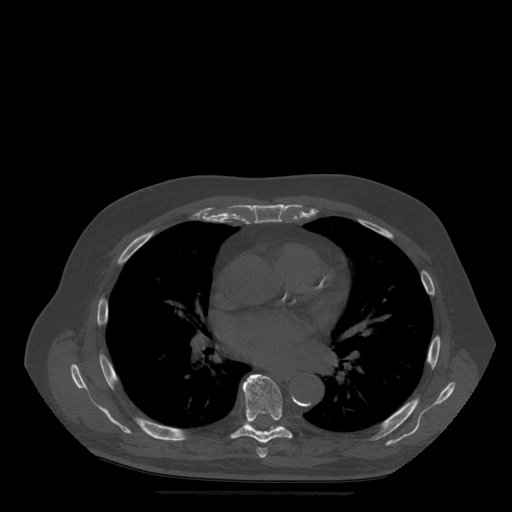
CT including the spine, one axial slice; bone window (W 1800 / L 400 HU); 512 × 512 image matrix, field of view 420 × 420 mm. Patient age 72 years. Case-level facts recorded for this patient, not image findings: primary cancer: prostate.
Outlined on this slice (semi-automatically segmented with operator editing):
- T6 vertebra: bounding box (x1, y1, x2, y2) in pixels: (244, 387, 268, 459)
- T7 vertebra: (231, 374, 293, 444)
- T8 vertebra: (248, 424, 255, 430)